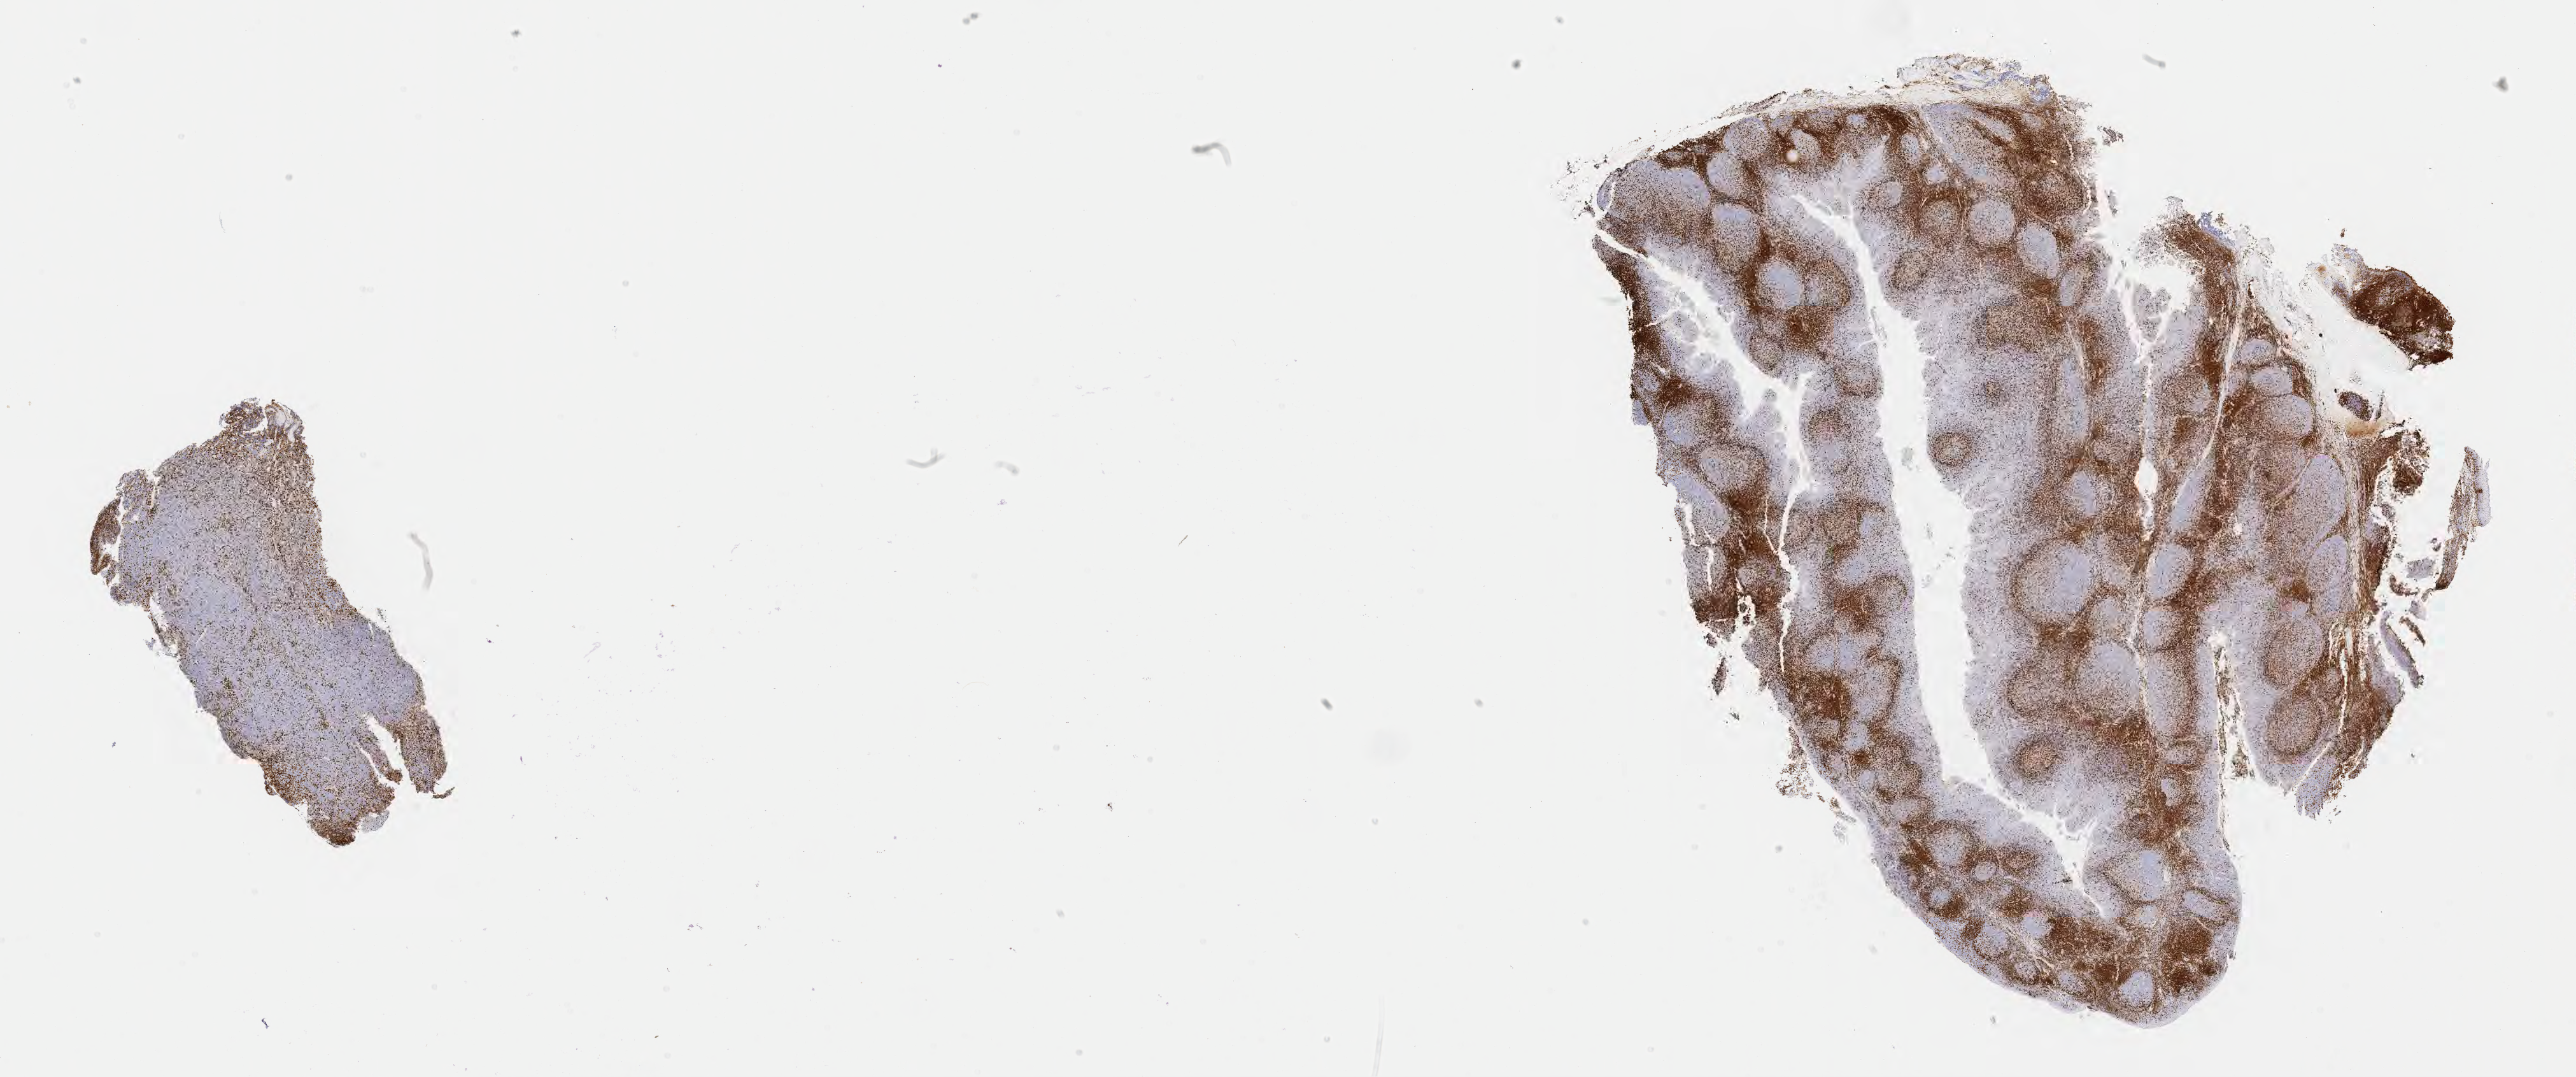
IHC for CD3, whole-slide image — whole scanned area (about 32.7 x 13.7 mm) shown as a low-resolution overview; specimen: tumor tissue; anatomic site: cranium. Patient male; aged 11.
• diagnosis: Diffuse large B-cell lymphoma, NOS